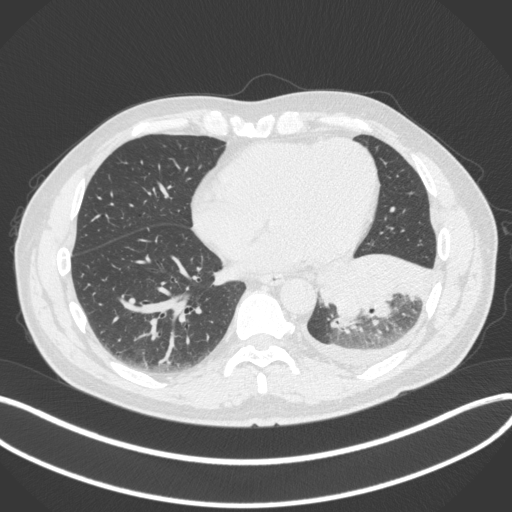
Chest CT, one axial slice. Slice 125 of 350 in the series (ordered by position). Reconstruction kernel B31f. 120 kVp. Lung window (W 1500 / L -600 HU). 512 × 512 image matrix, field of view 400 × 400 mm. Male patient, age 58 years. From the clinical record (not read from this slice): clinical TNM (as recorded): T3 N1 M1b; histopathological grade: G3.
Annotated regions visible in this slice (bounding box drawn by a radiologist):
- lung tumour (recorded histology: small cell carcinoma): bounding box (x1, y1, x2, y2) in pixels: (314, 243, 433, 324)